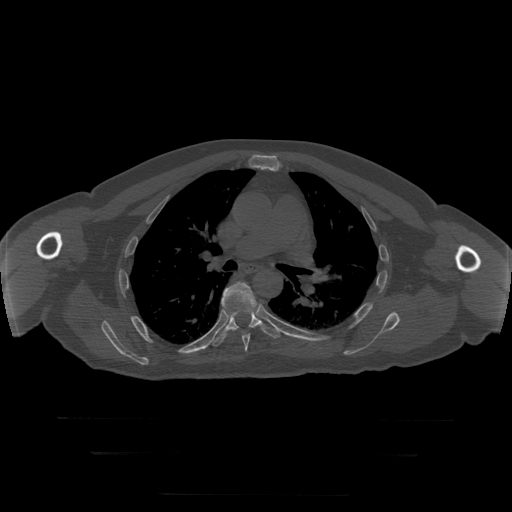
CT including the spine, one axial slice. Position 197 of 397 along the scan axis. Bone window (W 1800 / L 400 HU). 1.25 mm slice thickness. 512 × 512 image matrix. Patient age 73 years. From the clinical record (not read from this slice): primary cancer: prostate.
Structures marked on this image (semi-automatically segmented with operator editing):
- T6 vertebra: bounding box [x1, y1, x2, y2] px = [222, 282, 257, 352]
- T7 vertebra: [210, 312, 281, 347]